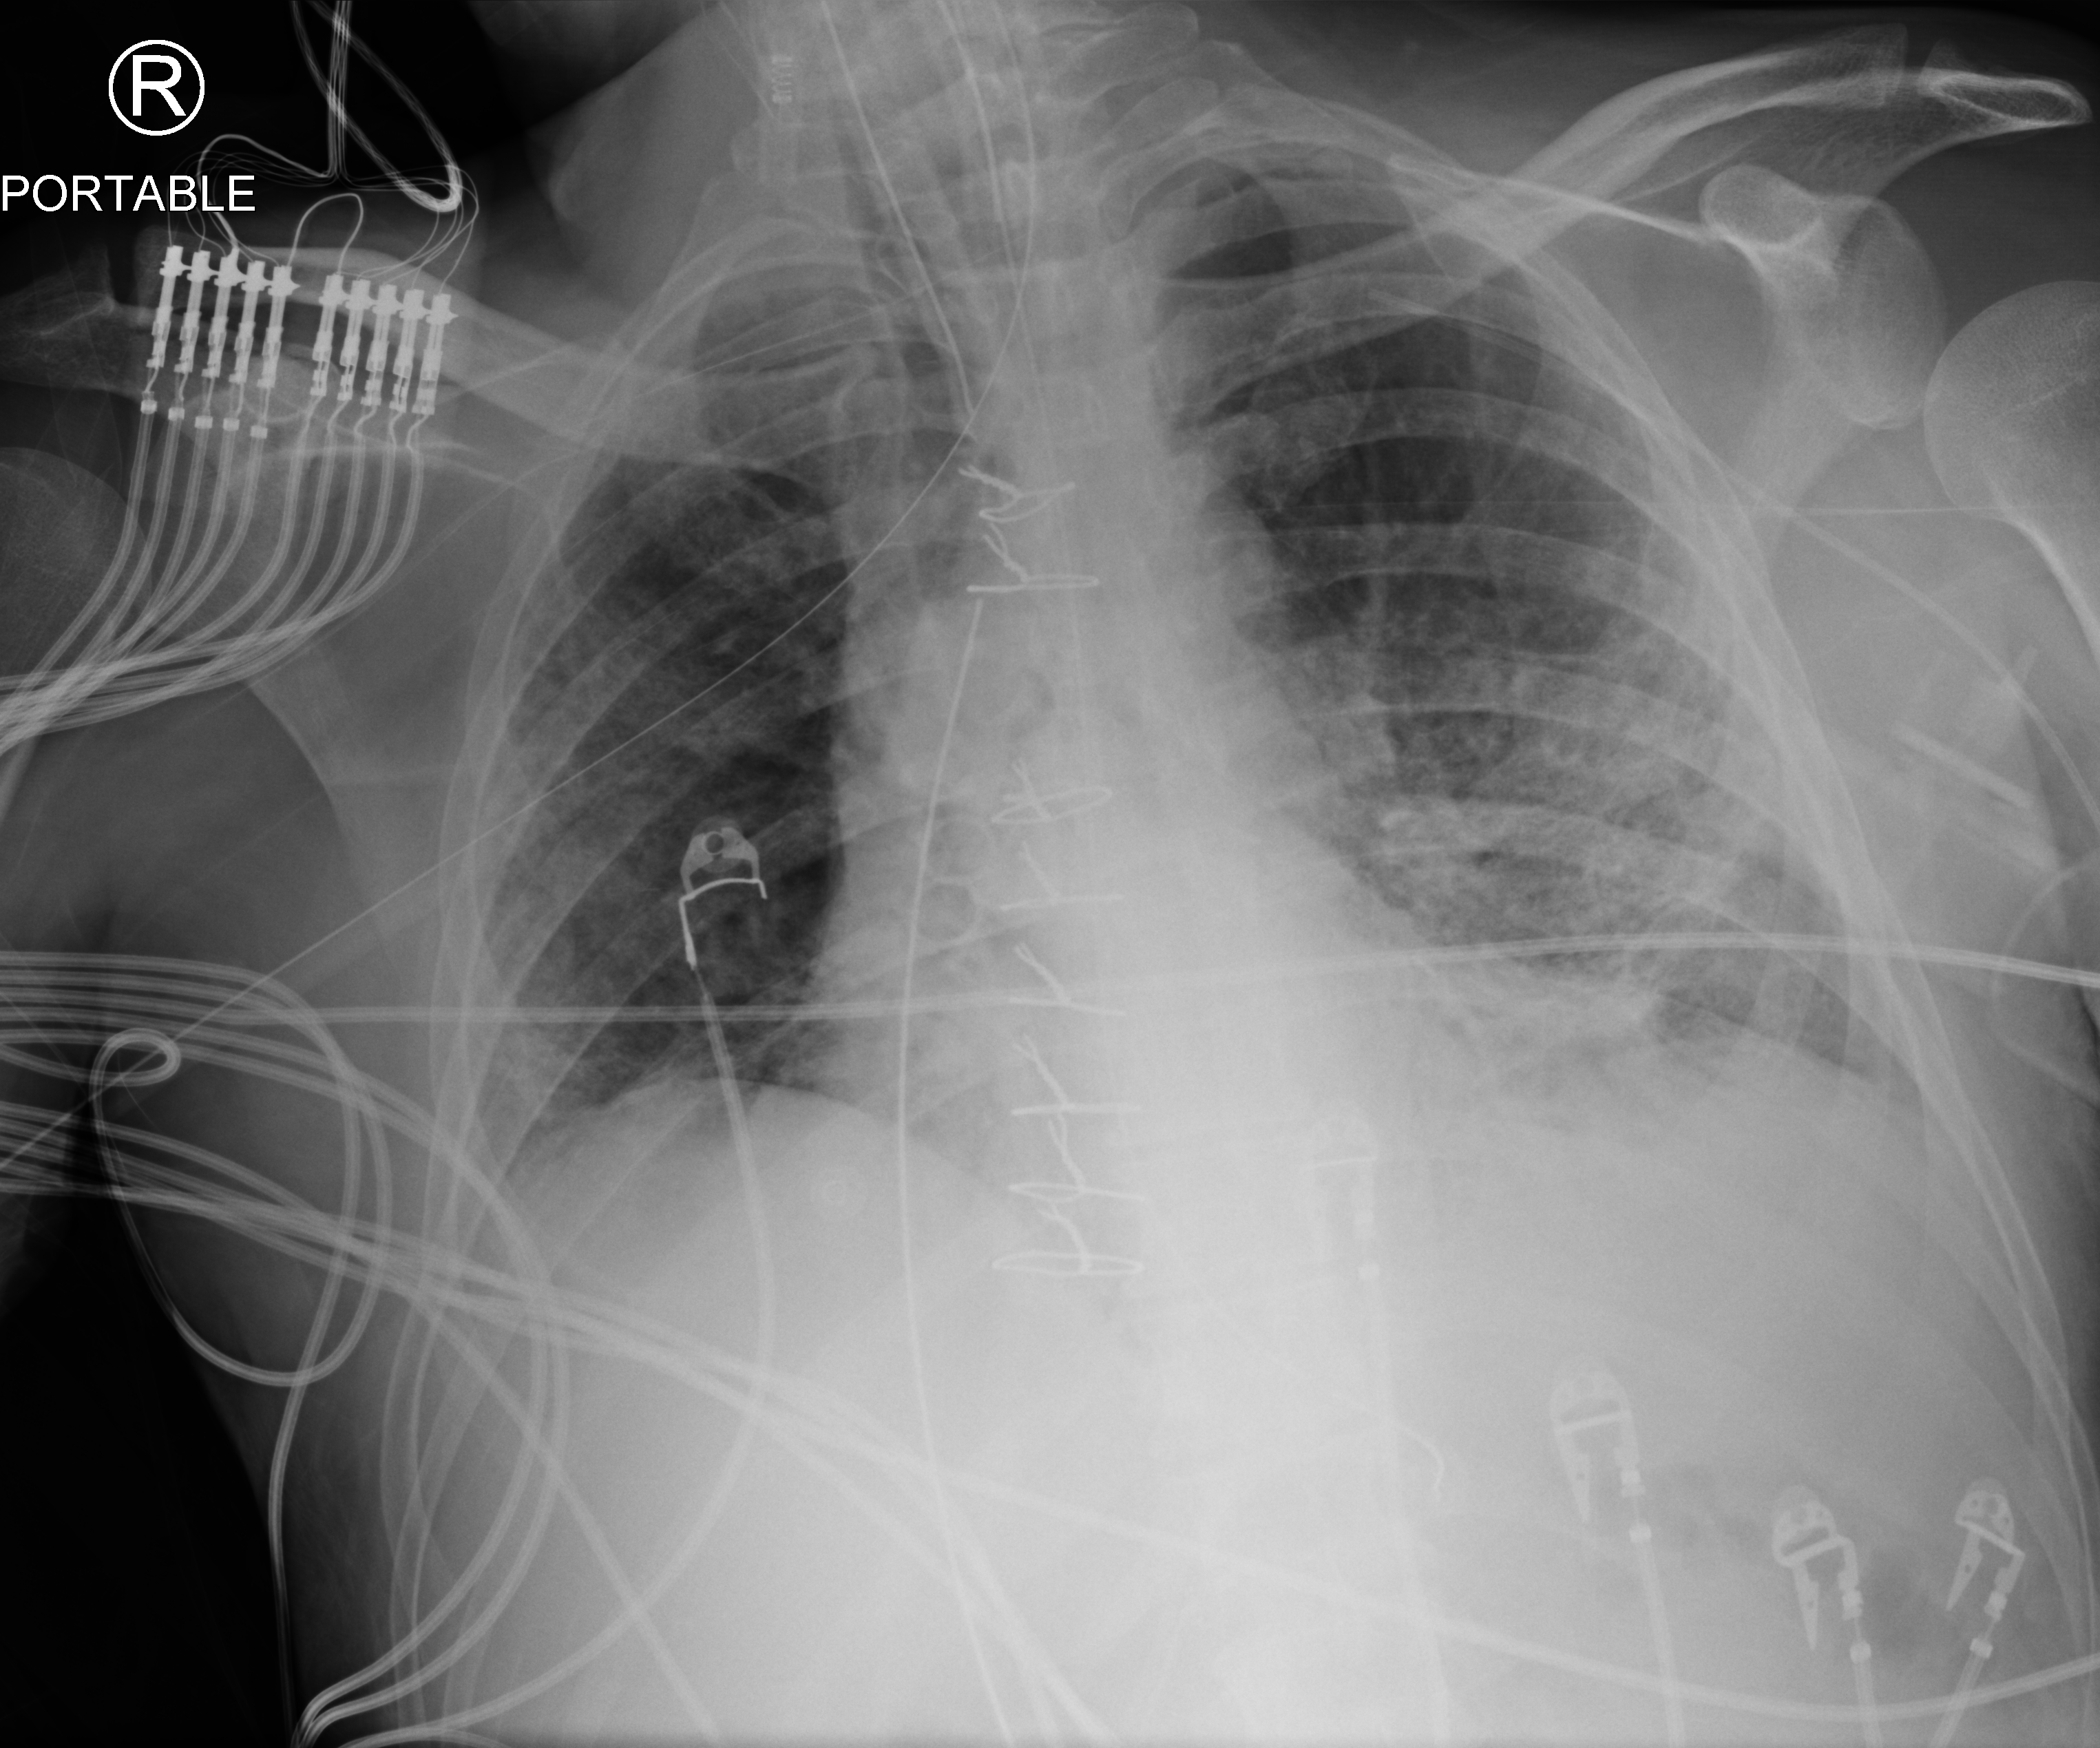
Chest X-ray (portable); anteroposterior (AP) projection. Male patient hospitalised with COVID-19, age 18–59 years.
Admission-level facts for this patient (not findings on this image; timing relative to this image not recorded): diabetes (admission record): yes; length of hospital stay: 63 days.